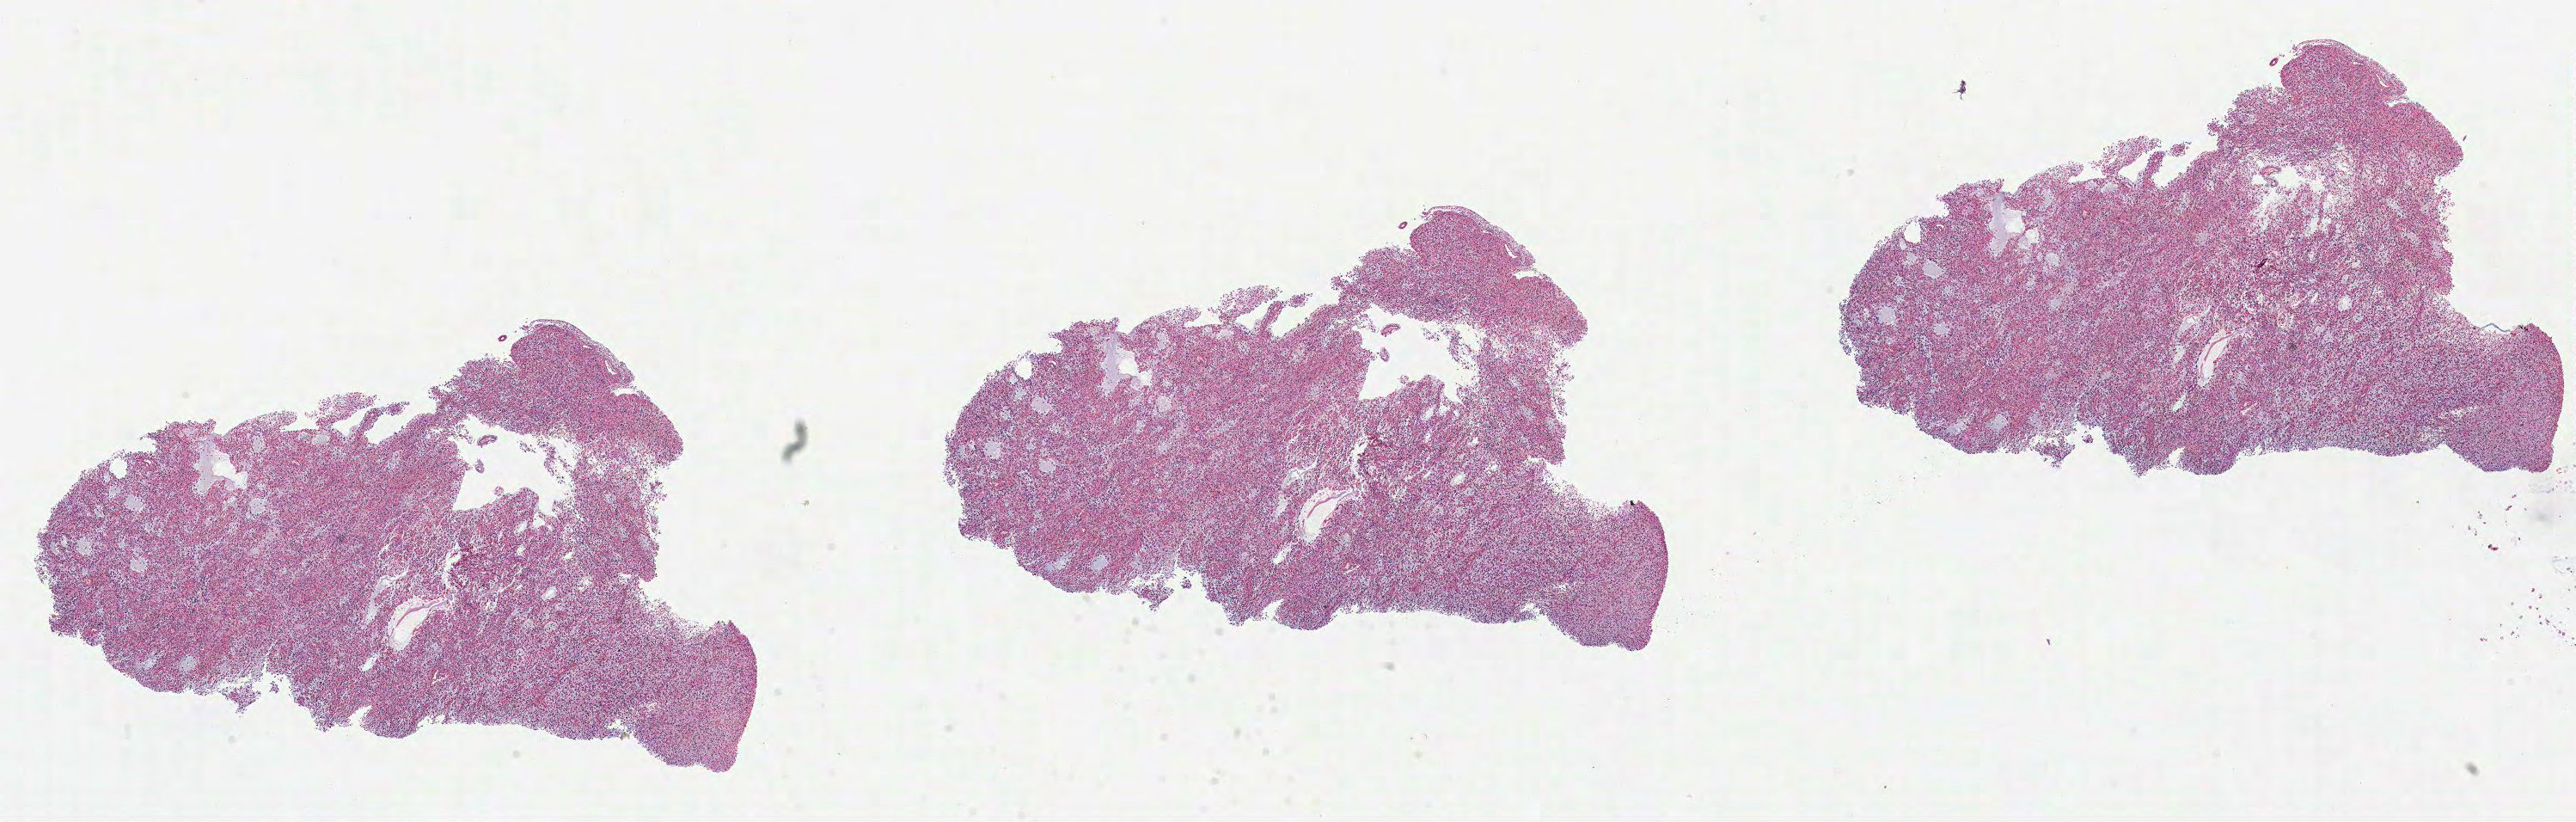
Whole-slide histology image, Hematoxylin and eosin (H&E) stained — whole scanned area (about 24.2 x 7.7 mm, from a 40x scan) shown as a low-resolution overview, formalin-fixed paraffin-embedded (FFPE) diagnostic section, primary tumour sample from the brain. Patient: male, age at initial diagnosis 25 years. Histologic grade: G3 (poorly differentiated).
Histologic diagnosis: Mixed glioma.